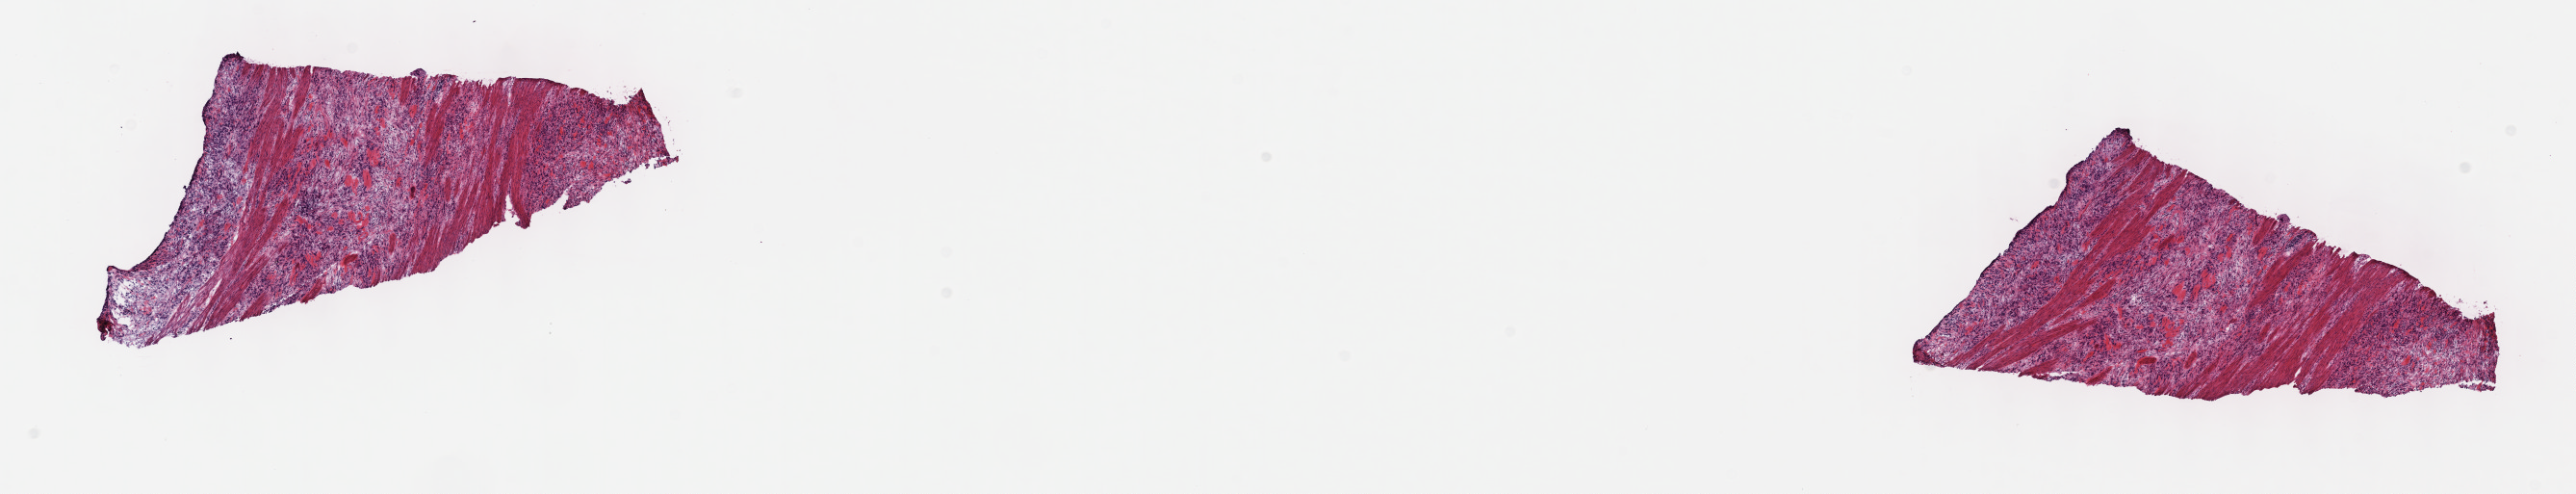
Hematoxylin and eosin (H&E) stained whole-slide image, shown as a low-resolution overview of the whole scanned area (about 21.6 x 4.1 mm, acquisition: 40x scan). Frozen section from the top of the tissue portion. Stomach, primary tumour sample. Patient: female, age at initial diagnosis 68 years. Histologic grade: G3 (poorly differentiated). Slide review estimates, as recorded: tumour cells 22%, tumour nuclei 65%, normal cells 0%, stromal cells 78%, necrosis 0%. Infiltration values recorded for this section: lymphocyte infiltration 20%, monocyte infiltration 2%, neutrophil infiltration 2%.
AJCC pathologic stage: IB (6th edition). Diagnosis: Carcinoma, diffuse type (fundus of stomach). Lymph nodes positive (case pathology): 0 of 23 examined.